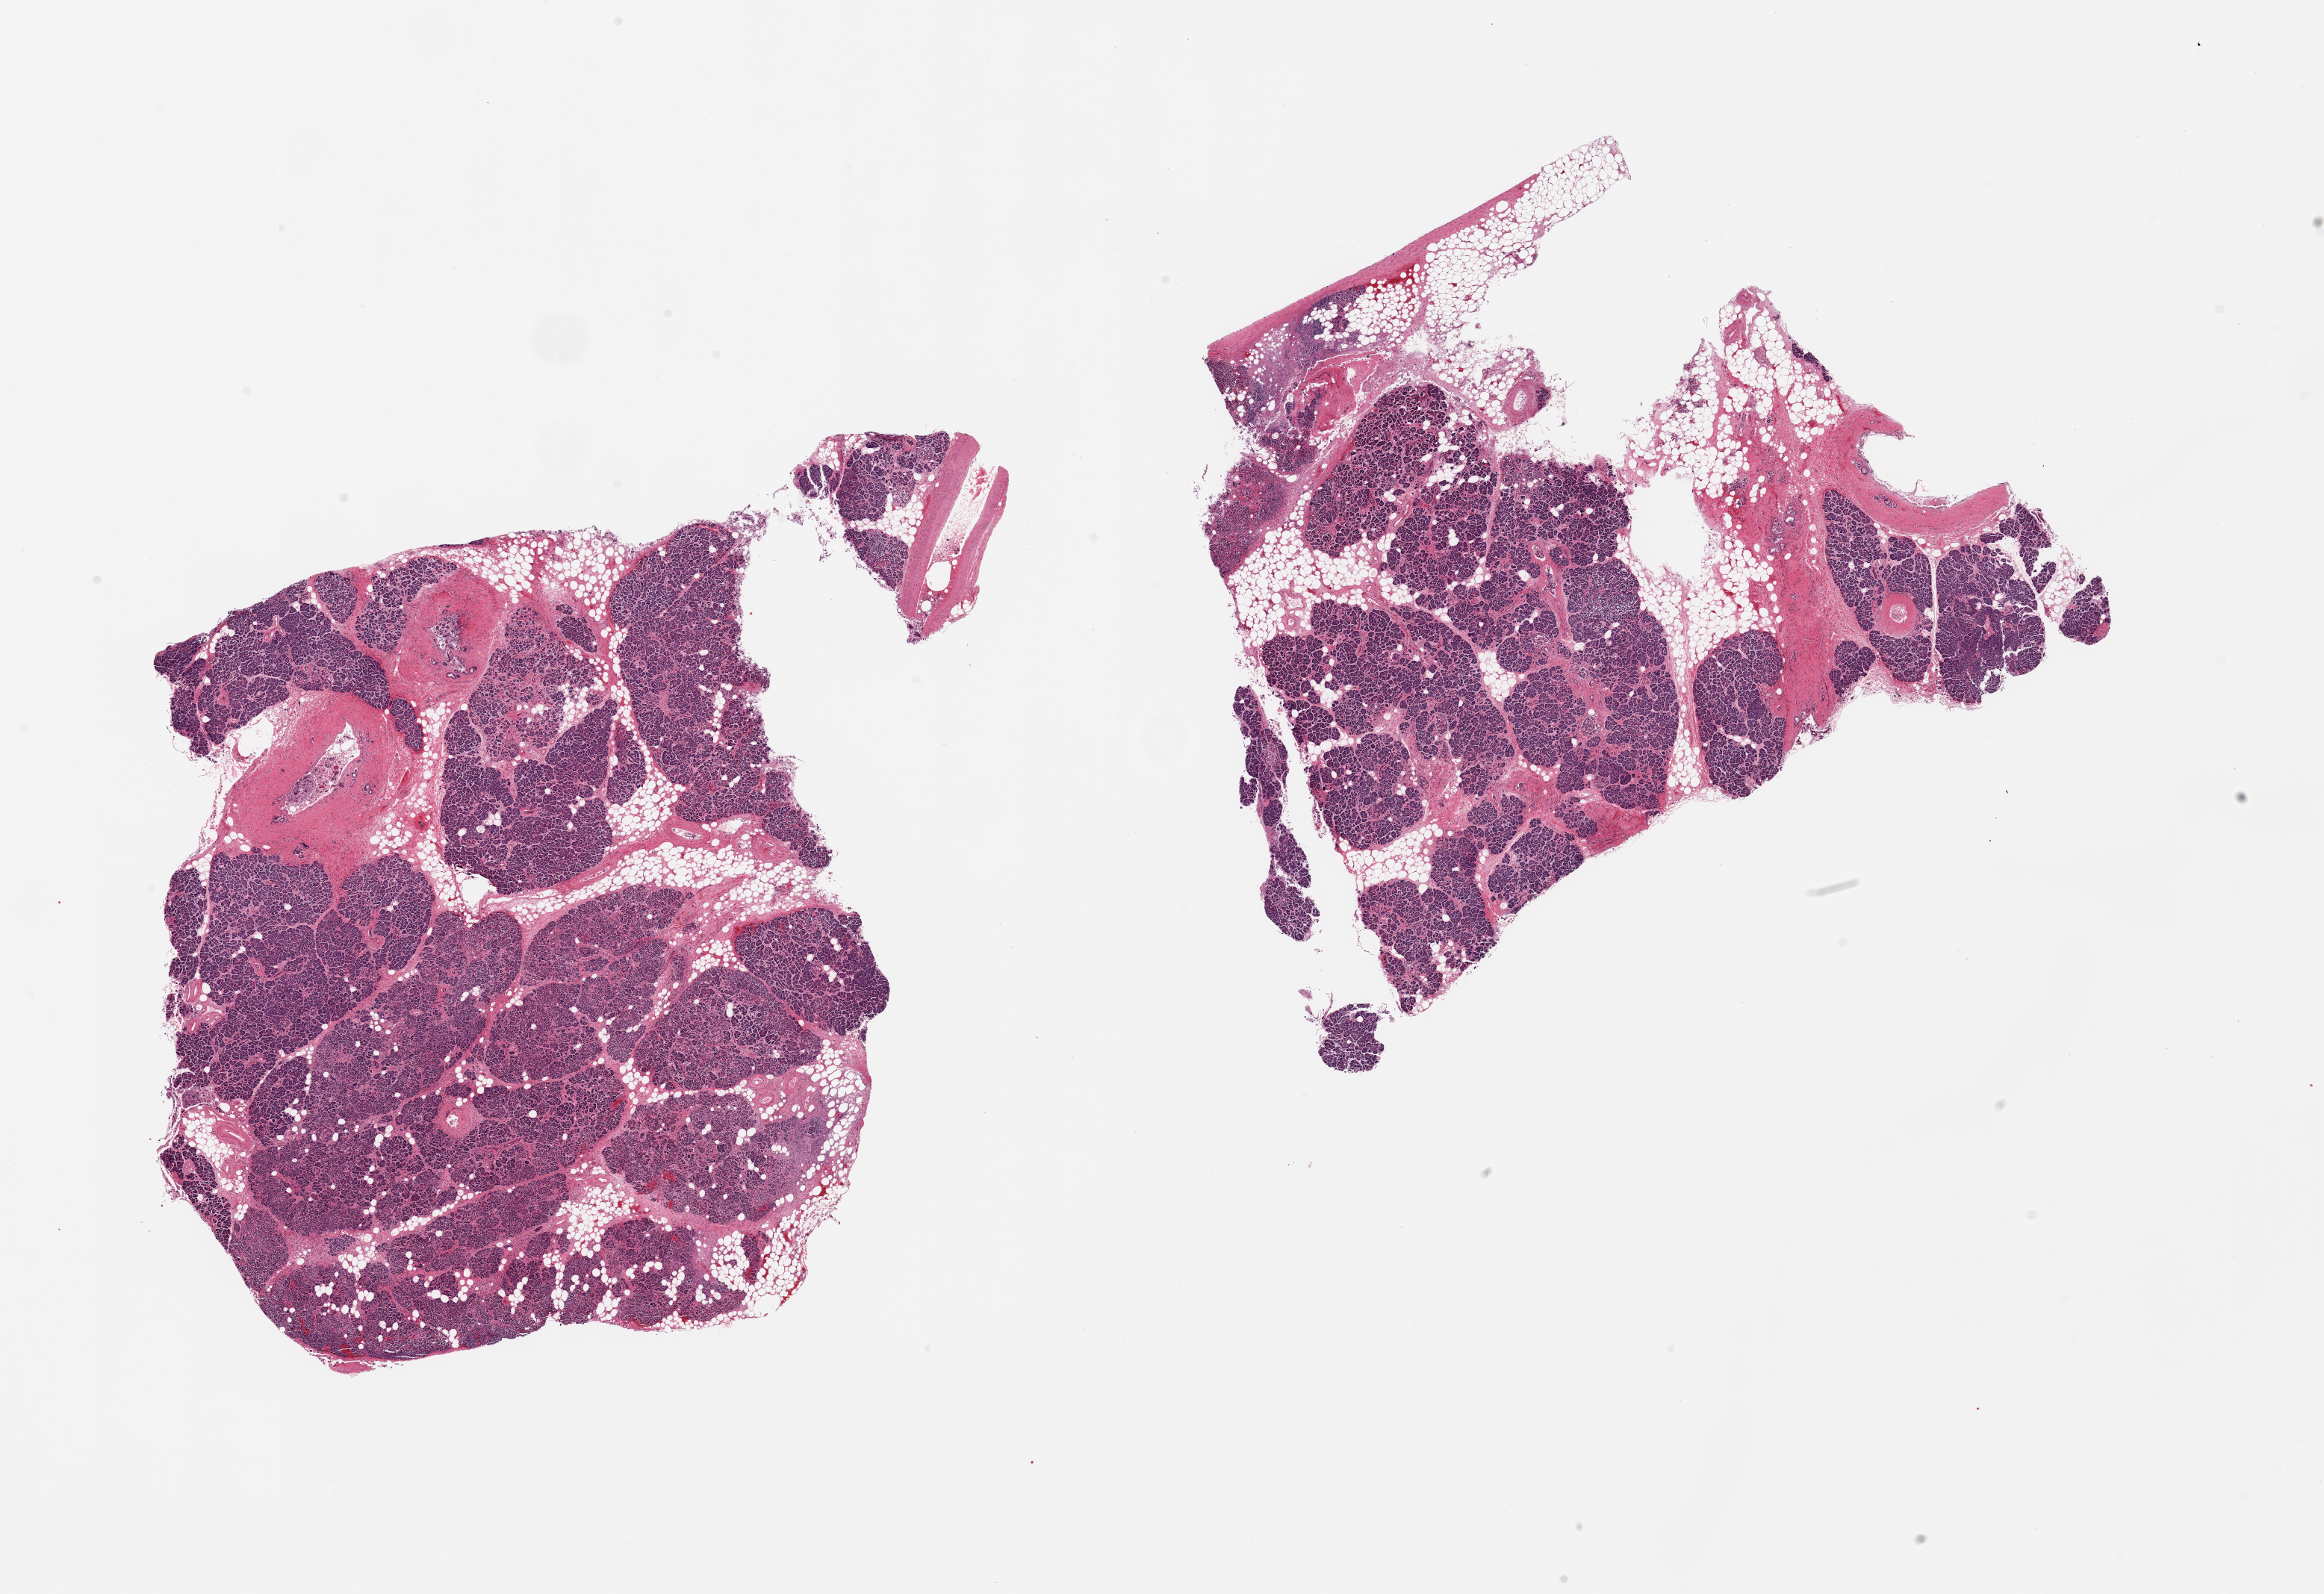
Haematoxylin and eosin whole-slide image, whole scanned area (about 24.6 x 16.9 mm, slide scanned at 20x) shown as a low-resolution overview; PAXgene-fixed, paraffin-embedded tissue; section of pancreas (target tissue); tissue donor sample. Male donor.
* reviewer comment on this tissue sample: 2 pieces, approaching score 2, Islets still visible but beginning to degrade, saponification advancing; ~20% adherent fat